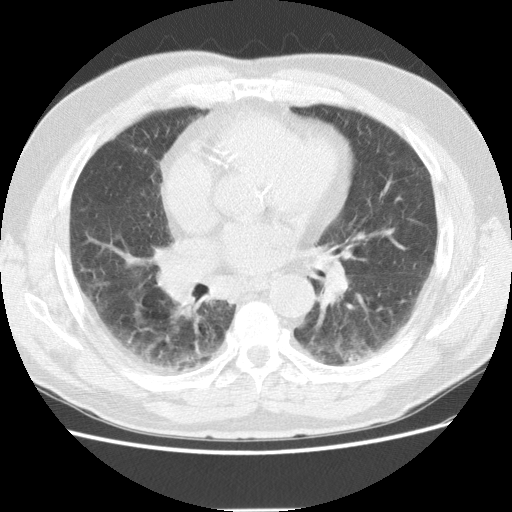
Chest CT (low-dose screening protocol), one axial image. Baseline annual screen. Lung window (W 1500 / L -600 HU). Male participant, aged 72 years at enrolment. Former smoker at enrolment.
Expert-annotated lung lesion, bounding box <148,238,194,274> (left, top, right, bottom; pixels). No non-calcified nodule or mass ≥4 mm was recorded by the screening reader at this exam. Later outcome: lung cancer diagnosed 163 days after this screen — adenocarcinoma, NOS, right middle lobe, stage IIIB (AJCC 6th edition), 27 mm at pathology.